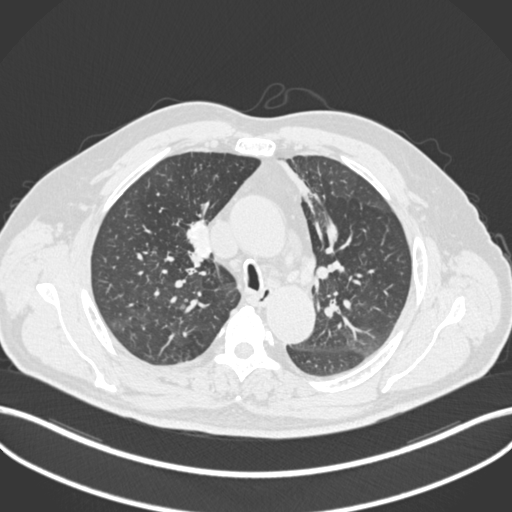
Chest CT, one axial slice. Position 135 of 255 along the scan axis. Reconstruction kernel B30f. Lung window (W 1500 / L -600 HU). 512 × 512 image matrix, field of view 400 × 400 mm. Male patient, age 60 years. Case-level facts recorded for this patient, not image findings: clinical TNM (as recorded): T1b N1 M0.
Outlined on this slice (bounding box drawn by a radiologist):
- lung tumour (recorded histology: squamous cell carcinoma): bounding box (x1, y1, x2, y2) in pixels: (183, 216, 218, 270)